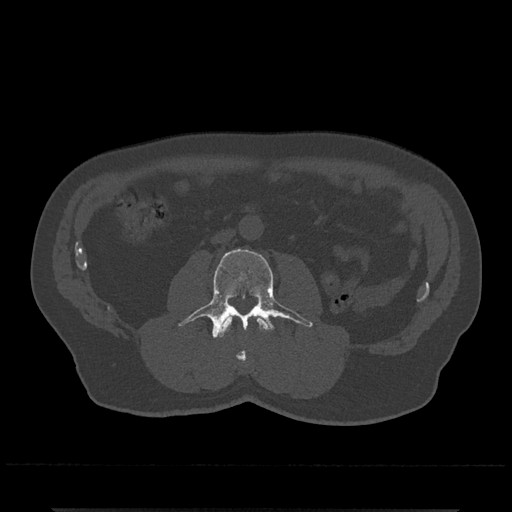
CT including the spine, one axial slice. Slice 233 of 797 in the series (ordered by position). Reconstruction kernel Br40s/3. 120 kVp. Bone window (W 1800 / L 400 HU). 0.5 mm slice thickness. 512 × 512 image matrix. Patient: male, 67 years. From the clinical record (not read from this slice): primary cancer: prostate.
Outlined on this slice (semi-automatically segmented with operator editing):
- L2 vertebra: bounding box [x1, y1, x2, y2] px = [218, 316, 269, 362]
- L3 vertebra: [178, 249, 313, 339]